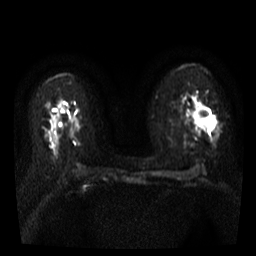
Breast MRI, one axial slice. Diffusion-weighted series; image 2 of 4 stored at this slice position (different b-values; order by instance number). 3 T. 5 mm slice thickness. 256 × 256 image matrix. Female patient.
Annotated regions visible in this slice (manually delineated by an expert):
- tumour on diffusion-weighted imaging: box from (x=192, y=106) to (x=216, y=130) px